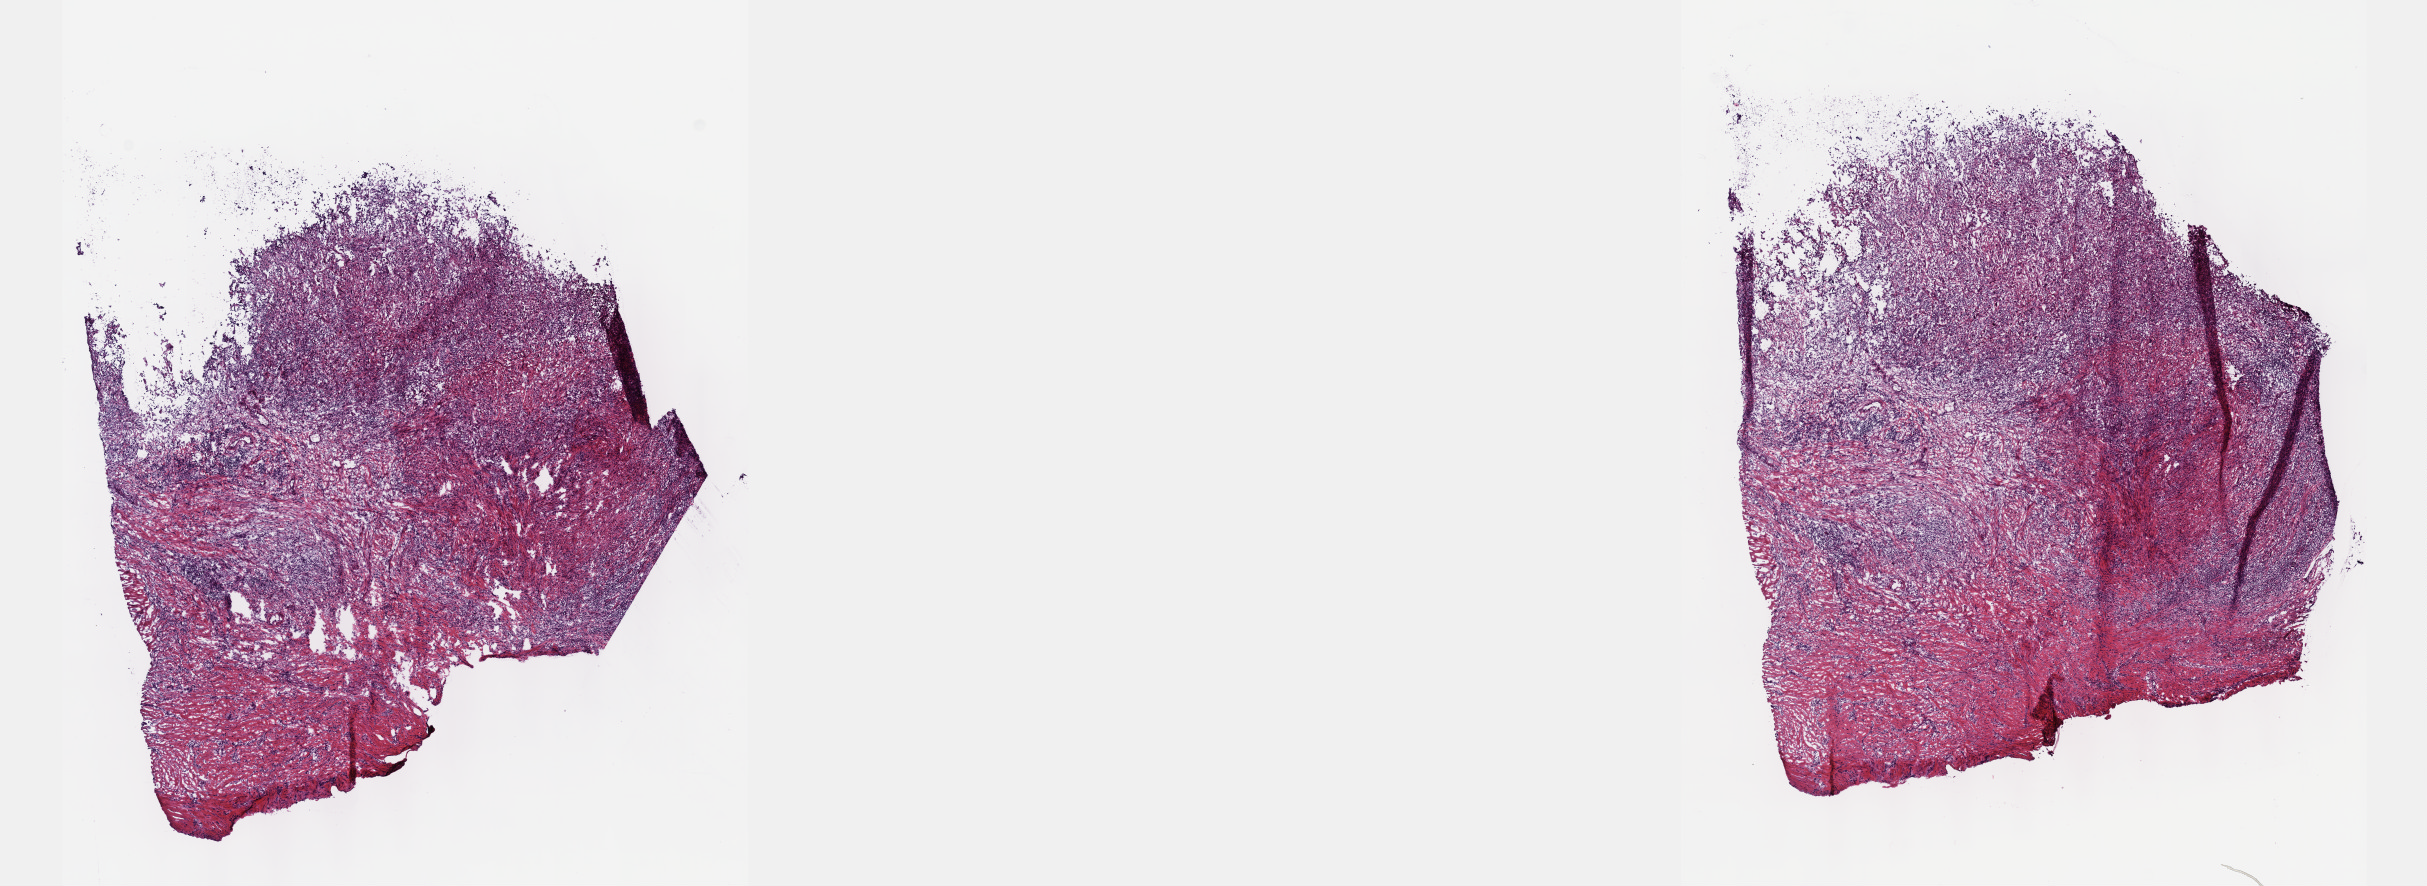
Whole-slide histology image, H&E-stained, a low-resolution overview of the entire scanned area, about 19.6 x 7.2 mm (from a 40x scan); frozen section; primary tumour sample from the mesothelium. Male, age 55 years at initial diagnosis. Slide review estimates, as recorded: tumour cells 100%, tumour nuclei 80%, normal cells 0%, stromal cells 0%, necrosis 0%. Infiltration values recorded for this section: lymphocyte infiltration 3%, monocyte infiltration 0%, neutrophil infiltration 0%.
Diagnosis: Fibrous mesothelioma, malignant. TNM: T2 N2 MX. AJCC pathologic stage: III (6th edition).